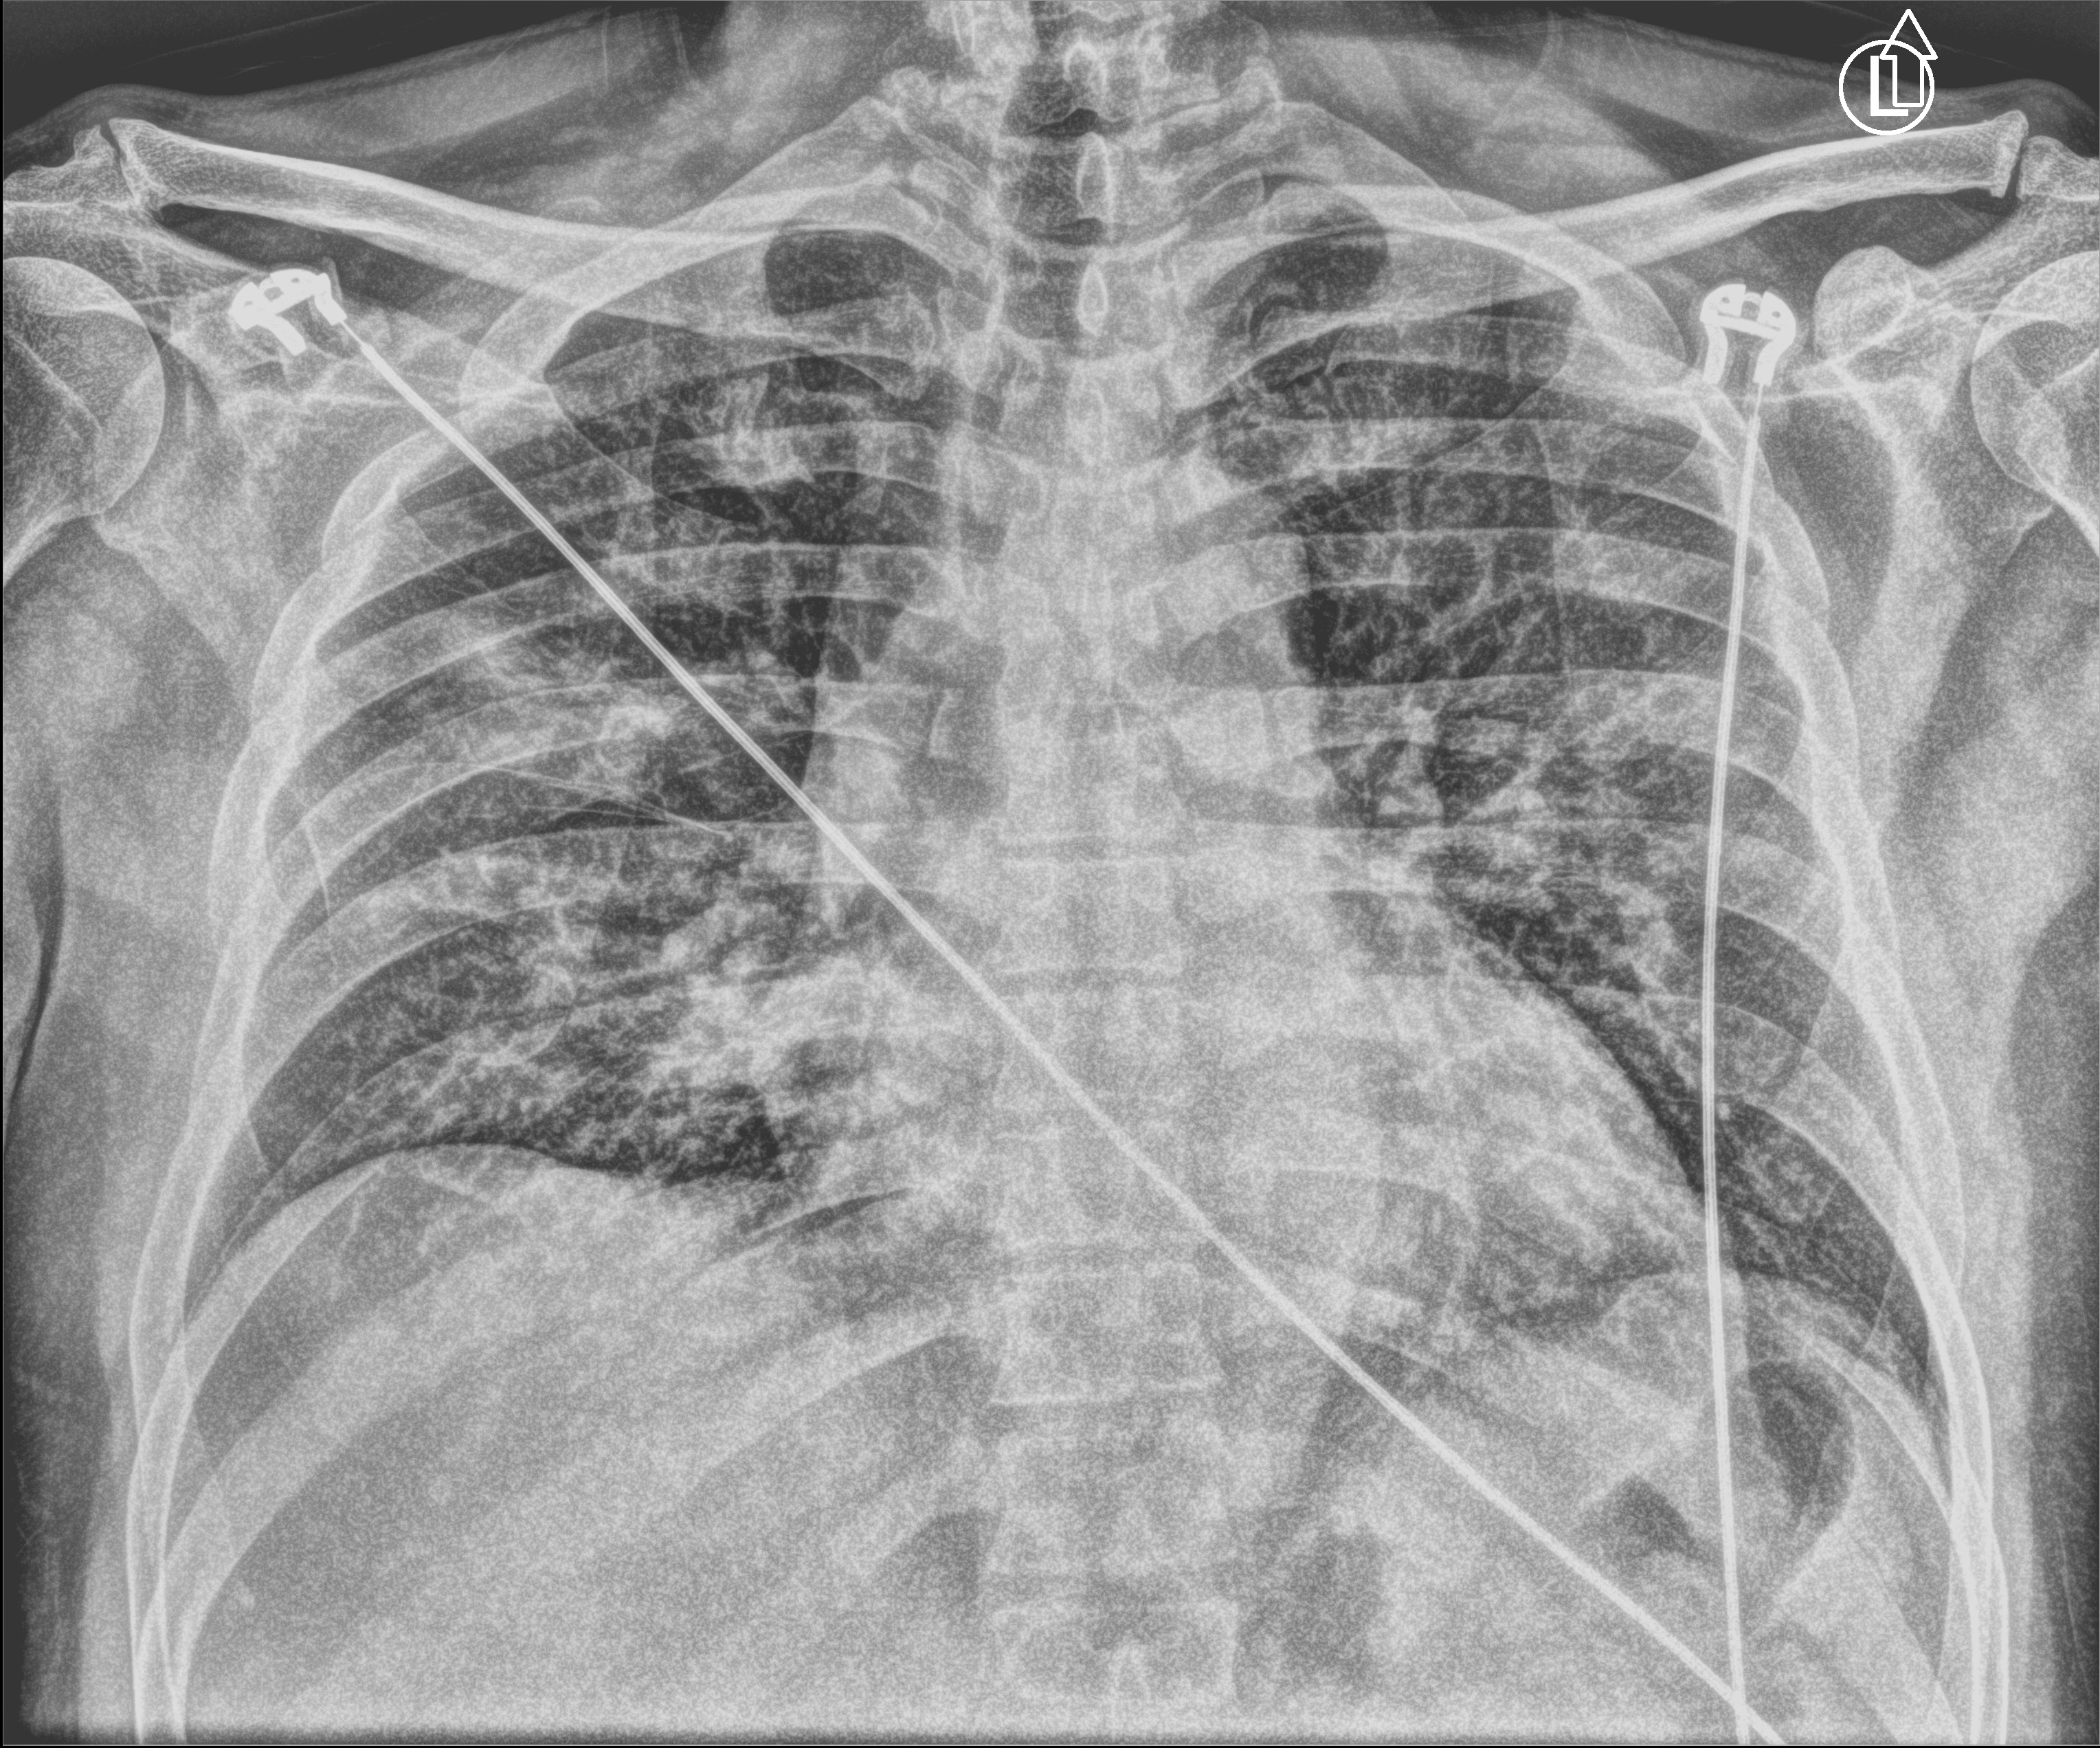
Portable chest radiograph; anteroposterior (AP) projection. Patient hospitalised with COVID-19; male, aged 60–74 years.
From the hospital-stay record, not from the radiograph (when in the stay this image was taken is not recorded):
- admitted to intensive care during this hospital stay: no
- mechanically ventilated during this hospital stay: no